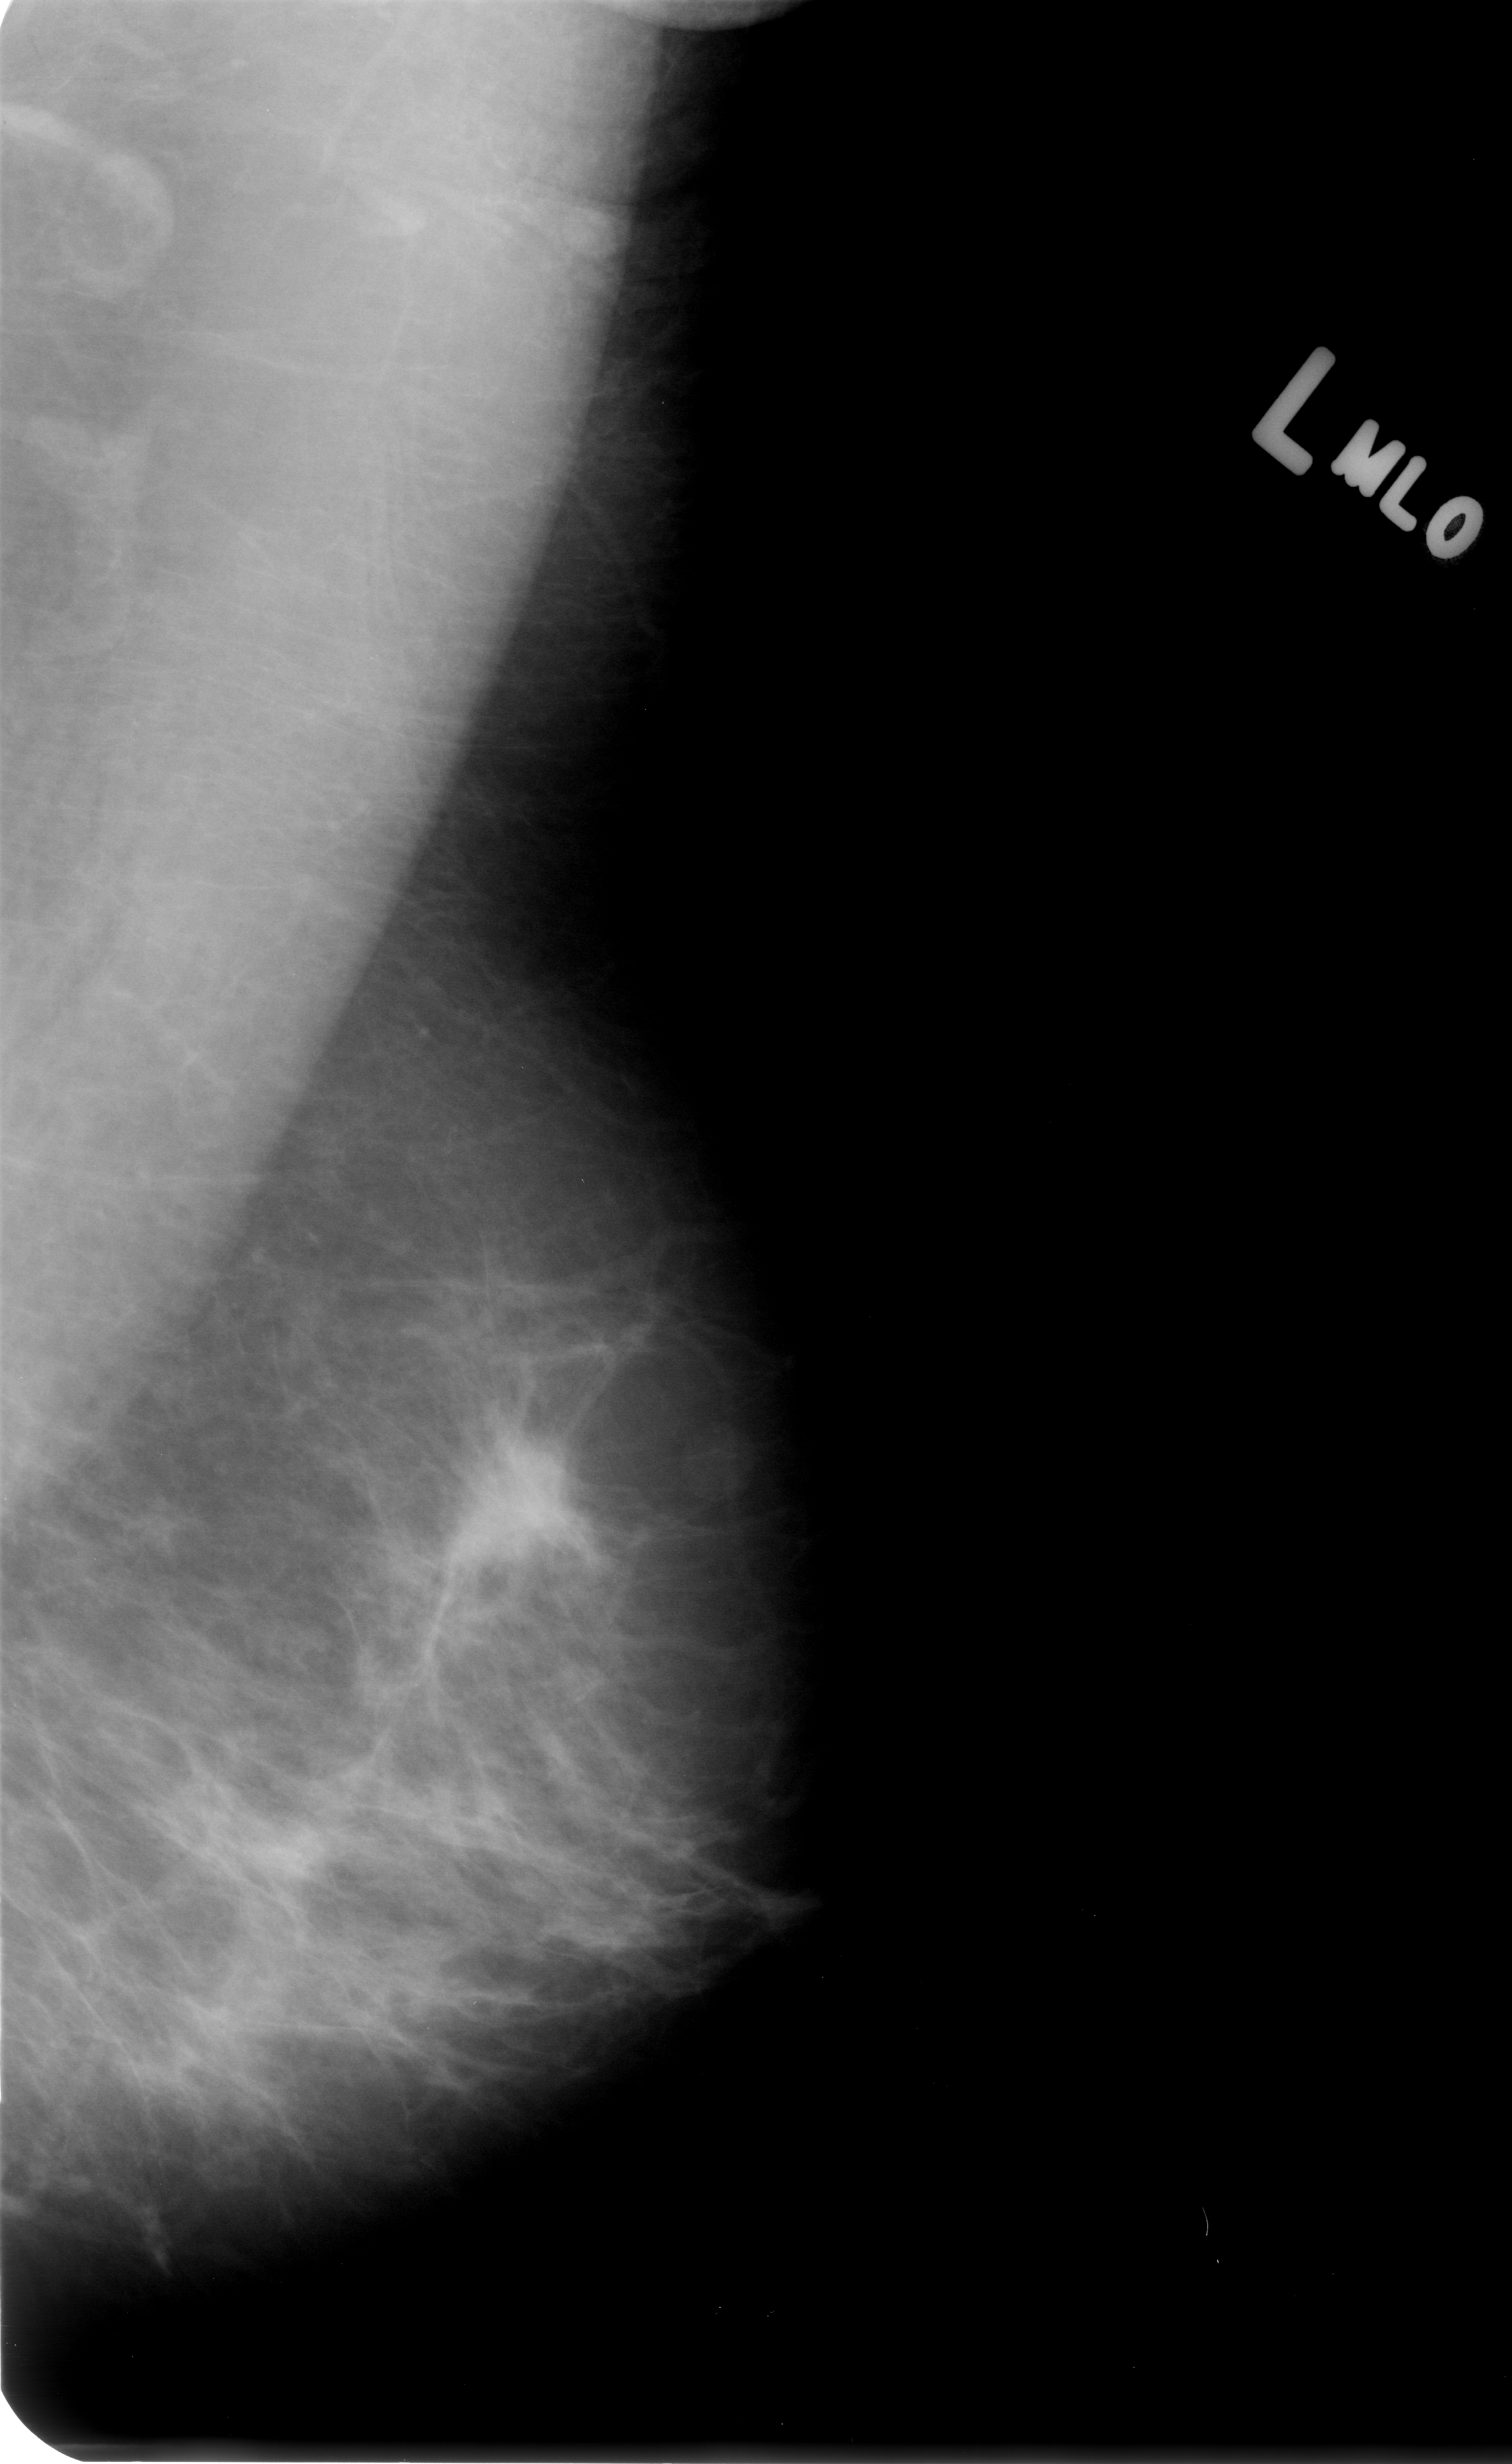
Scanned film-screen mammogram; left breast; MLO view; breast composition: heterogeneously dense (BI-RADS density category 3 of 4).
Mass, shape irregular / architectural distortion, margins spiculated; BI-RADS assessment category 4; pathology (as recorded): malignant.